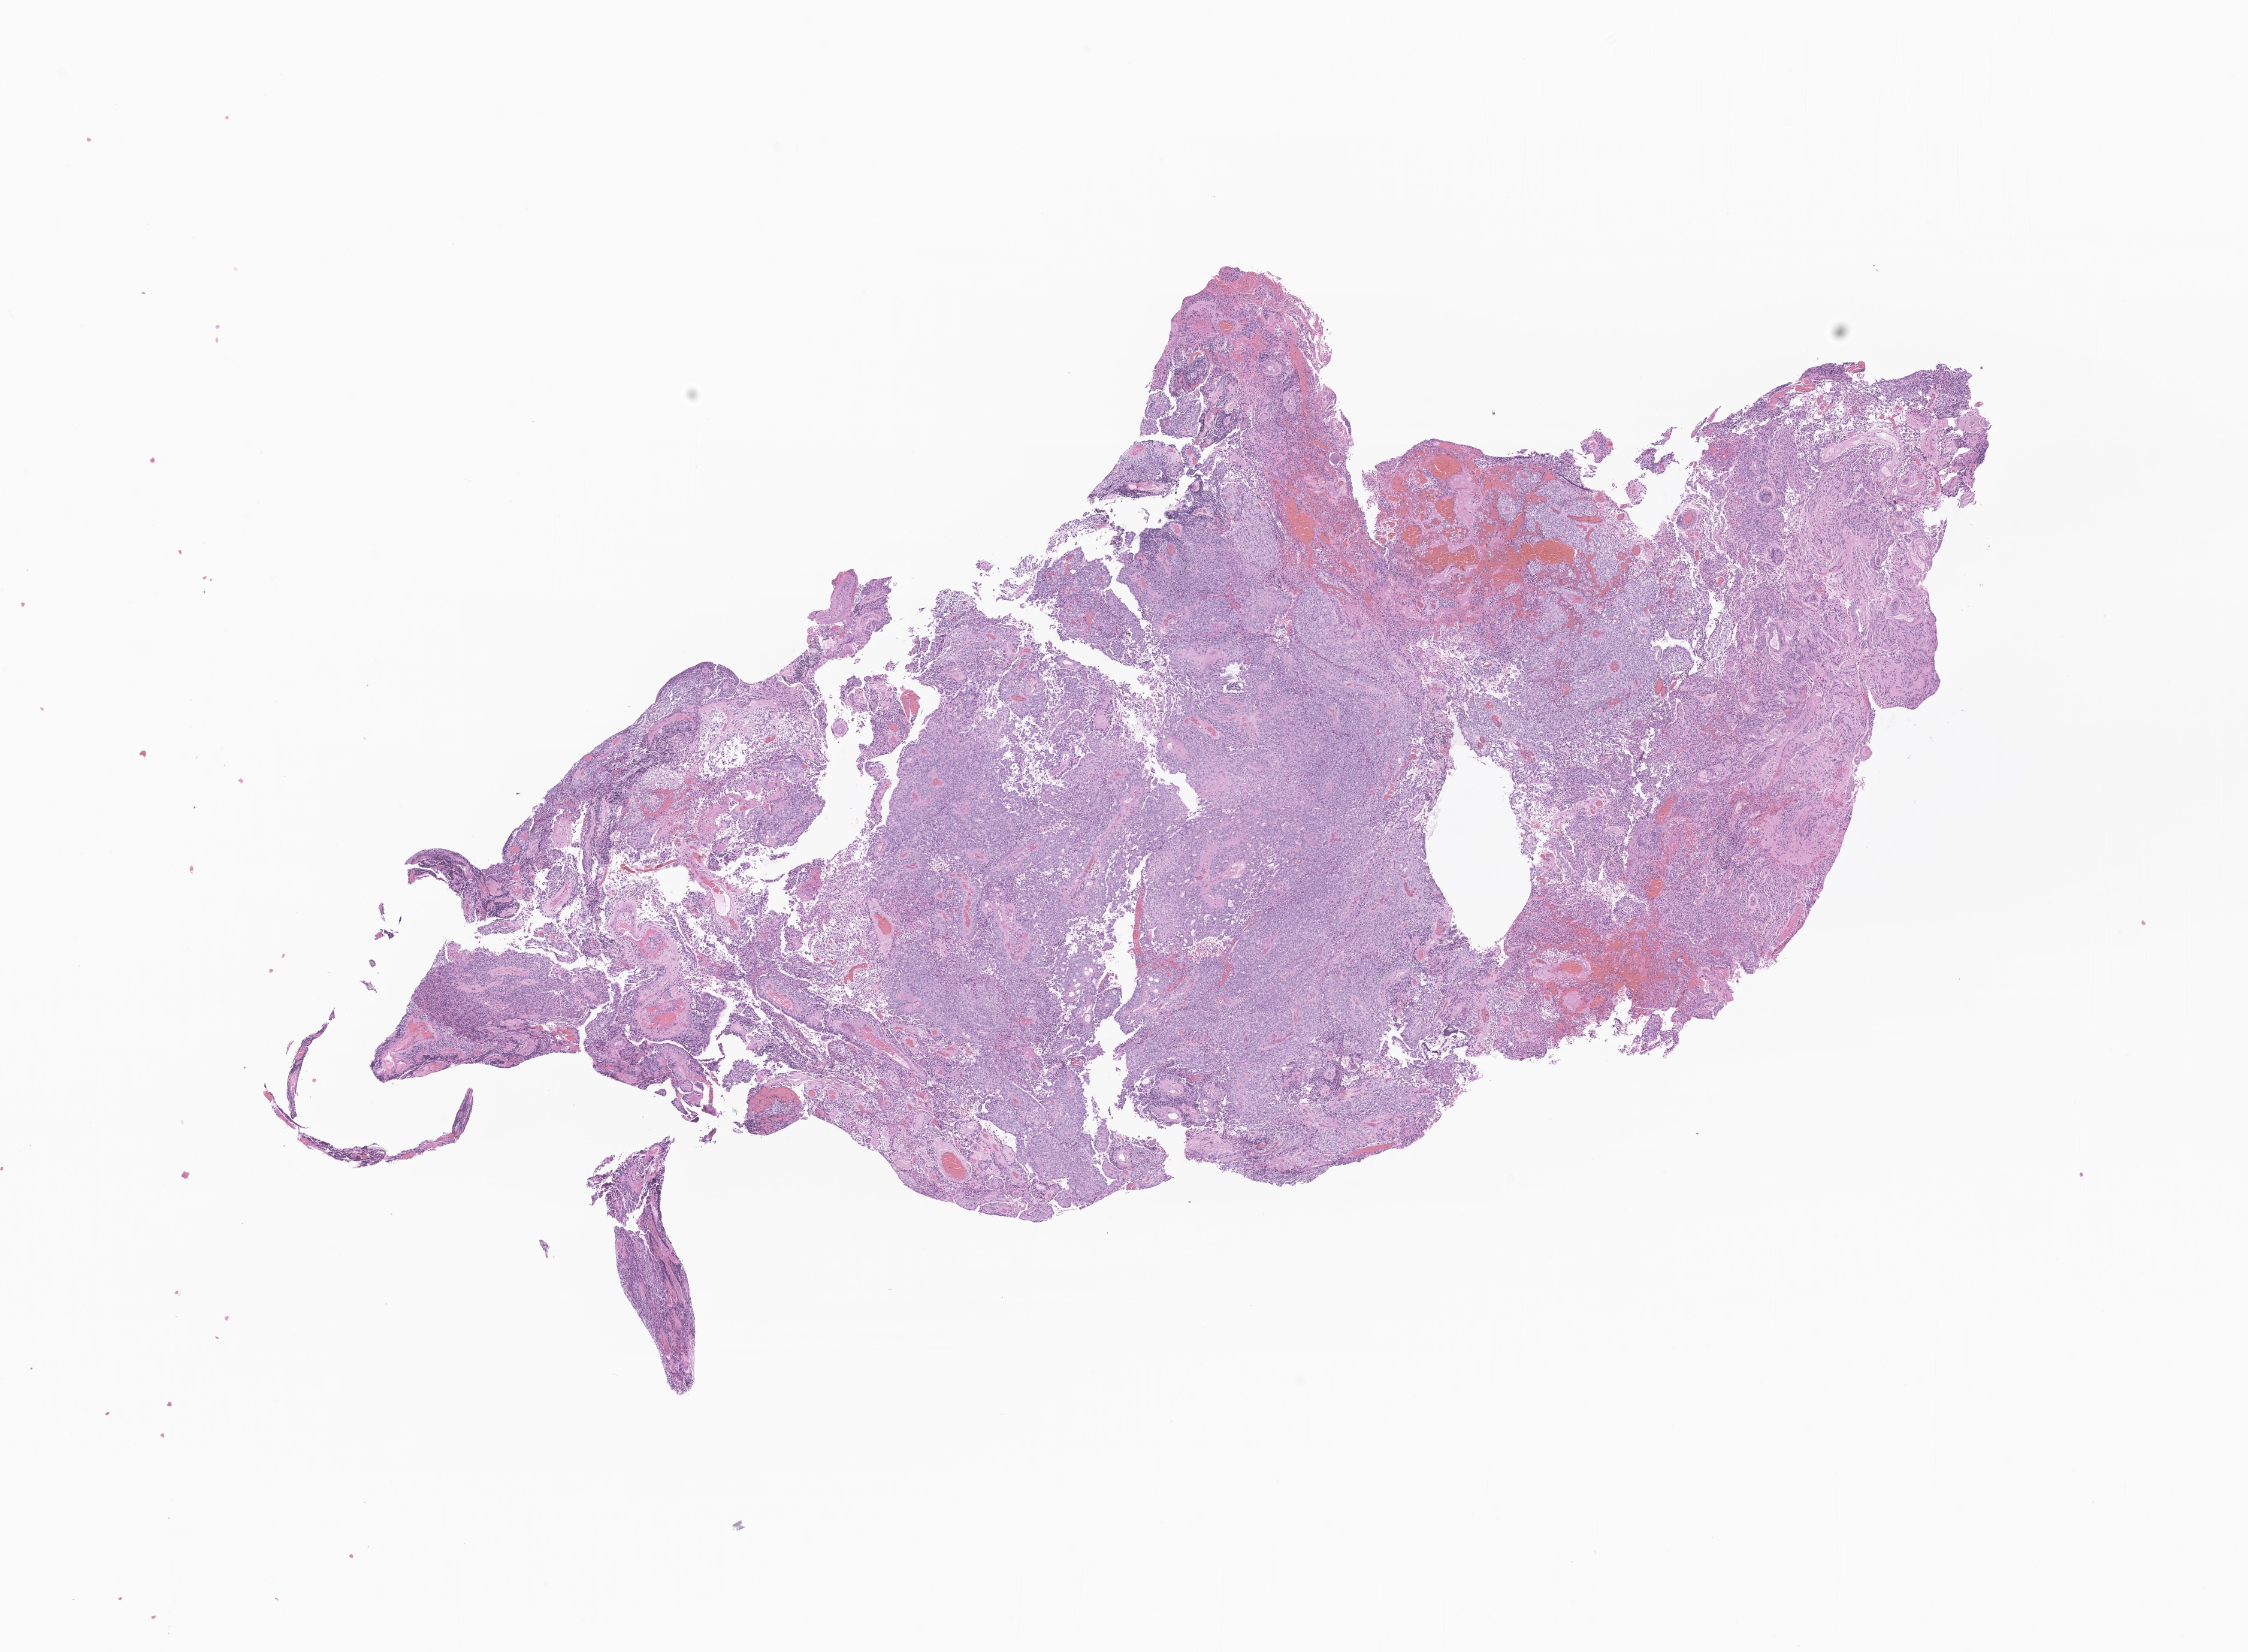
H&E whole-slide image of tumor tissue from the brain — whole scanned area (about 15.8 x 11.6 mm) shown as a low-resolution overview, formalin-fixed paraffin-embedded section. Female patient, age 180 months (15 years).
Diagnosis: Ependymoma, NOS.